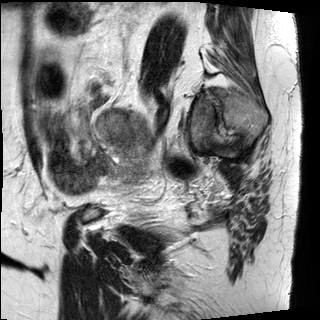
Pelvic MRI for cervical cancer, one sagittal slice; slice 24 of 30 in the series (ordered by position); T2-weighted; 1.5 T; TE 89 ms, TR 2930 ms; 4 mm slice thickness; 320 × 320 image matrix. Patient: female, 62 years.
Outlined on this slice (manually delineated by an expert):
- uterus and cervix: box from (x=97, y=109) to (x=154, y=152) px